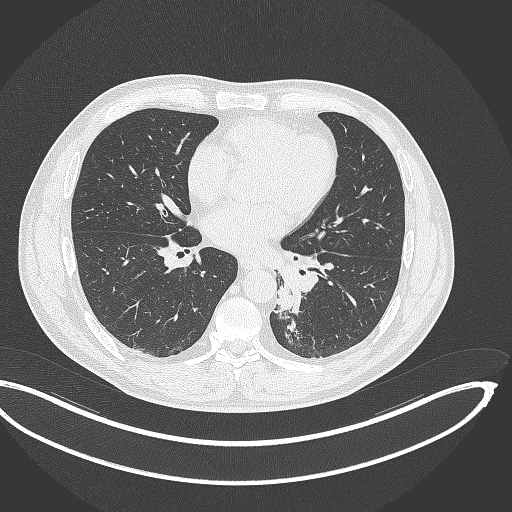
Chest CT, one axial slice; position 160 of 362 along the scan axis; reconstruction kernel B70f; lung window (W 1500 / L -600 HU); 1 mm slice thickness; 512 × 512 image matrix, field of view 442 × 442 mm. Patient: male, 50 years. Case-level facts recorded for this patient, not image findings: clinical TNM (as recorded): T2a N3 M0.
Annotated regions visible in this slice (bounding box drawn by a radiologist):
- lung tumour (recorded histology: squamous cell carcinoma): bounding box (x1, y1, x2, y2) in pixels: (274, 279, 296, 316)